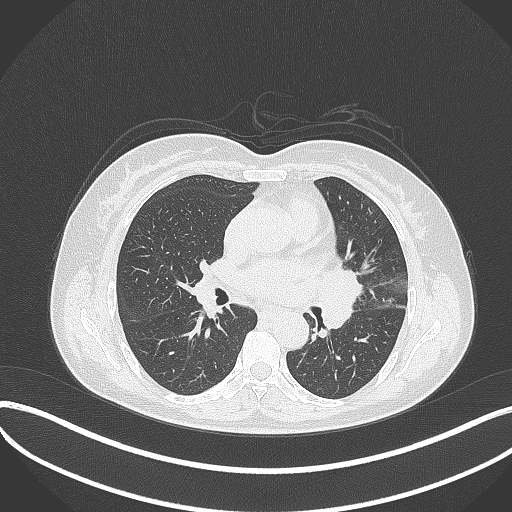
Chest CT, one axial slice. Position 186 of 373 along the scan axis. Reconstruction kernel B70f. 120 kVp. Lung window (W 1500 / L -600 HU). 1 mm slice thickness. 512 × 512 image matrix, field of view 400 × 400 mm. Patient: female, 54 years. Case-level facts recorded for this patient, not image findings: clinical TNM (as recorded): T2a N1 M0; histopathological grade: G3.
Outlined on this slice (bounding box drawn by a radiologist):
- lung tumour (recorded histology: small cell carcinoma): bounding box <319,265,369,336> (left, top, right, bottom; pixels)